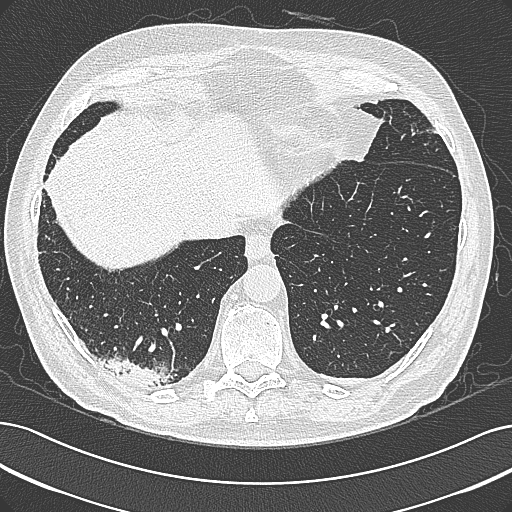
Low-dose screening chest CT, axial slice. Baseline annual screen. Lung window (W 1500 / L -600 HU). 1 mm slice thickness. Slice 230 of 355 in the series. 512 × 512 image matrix, field of view 362 × 362 mm. Male participant, aged 68 years at enrolment. Former smoker at enrolment.
• Expert-annotated lung lesion, bounding box <97,341,184,402> (left, top, right, bottom; pixels).
• Screening reader's record for this exam: no non-calcified nodule ≥4 mm recorded.
• Lung cancer was diagnosed 154 days after this screen: mucinous adenocarcinoma, right lower lobe, well differentiated (G1), stage IB (AJCC 6th edition), 50 mm at pathology.